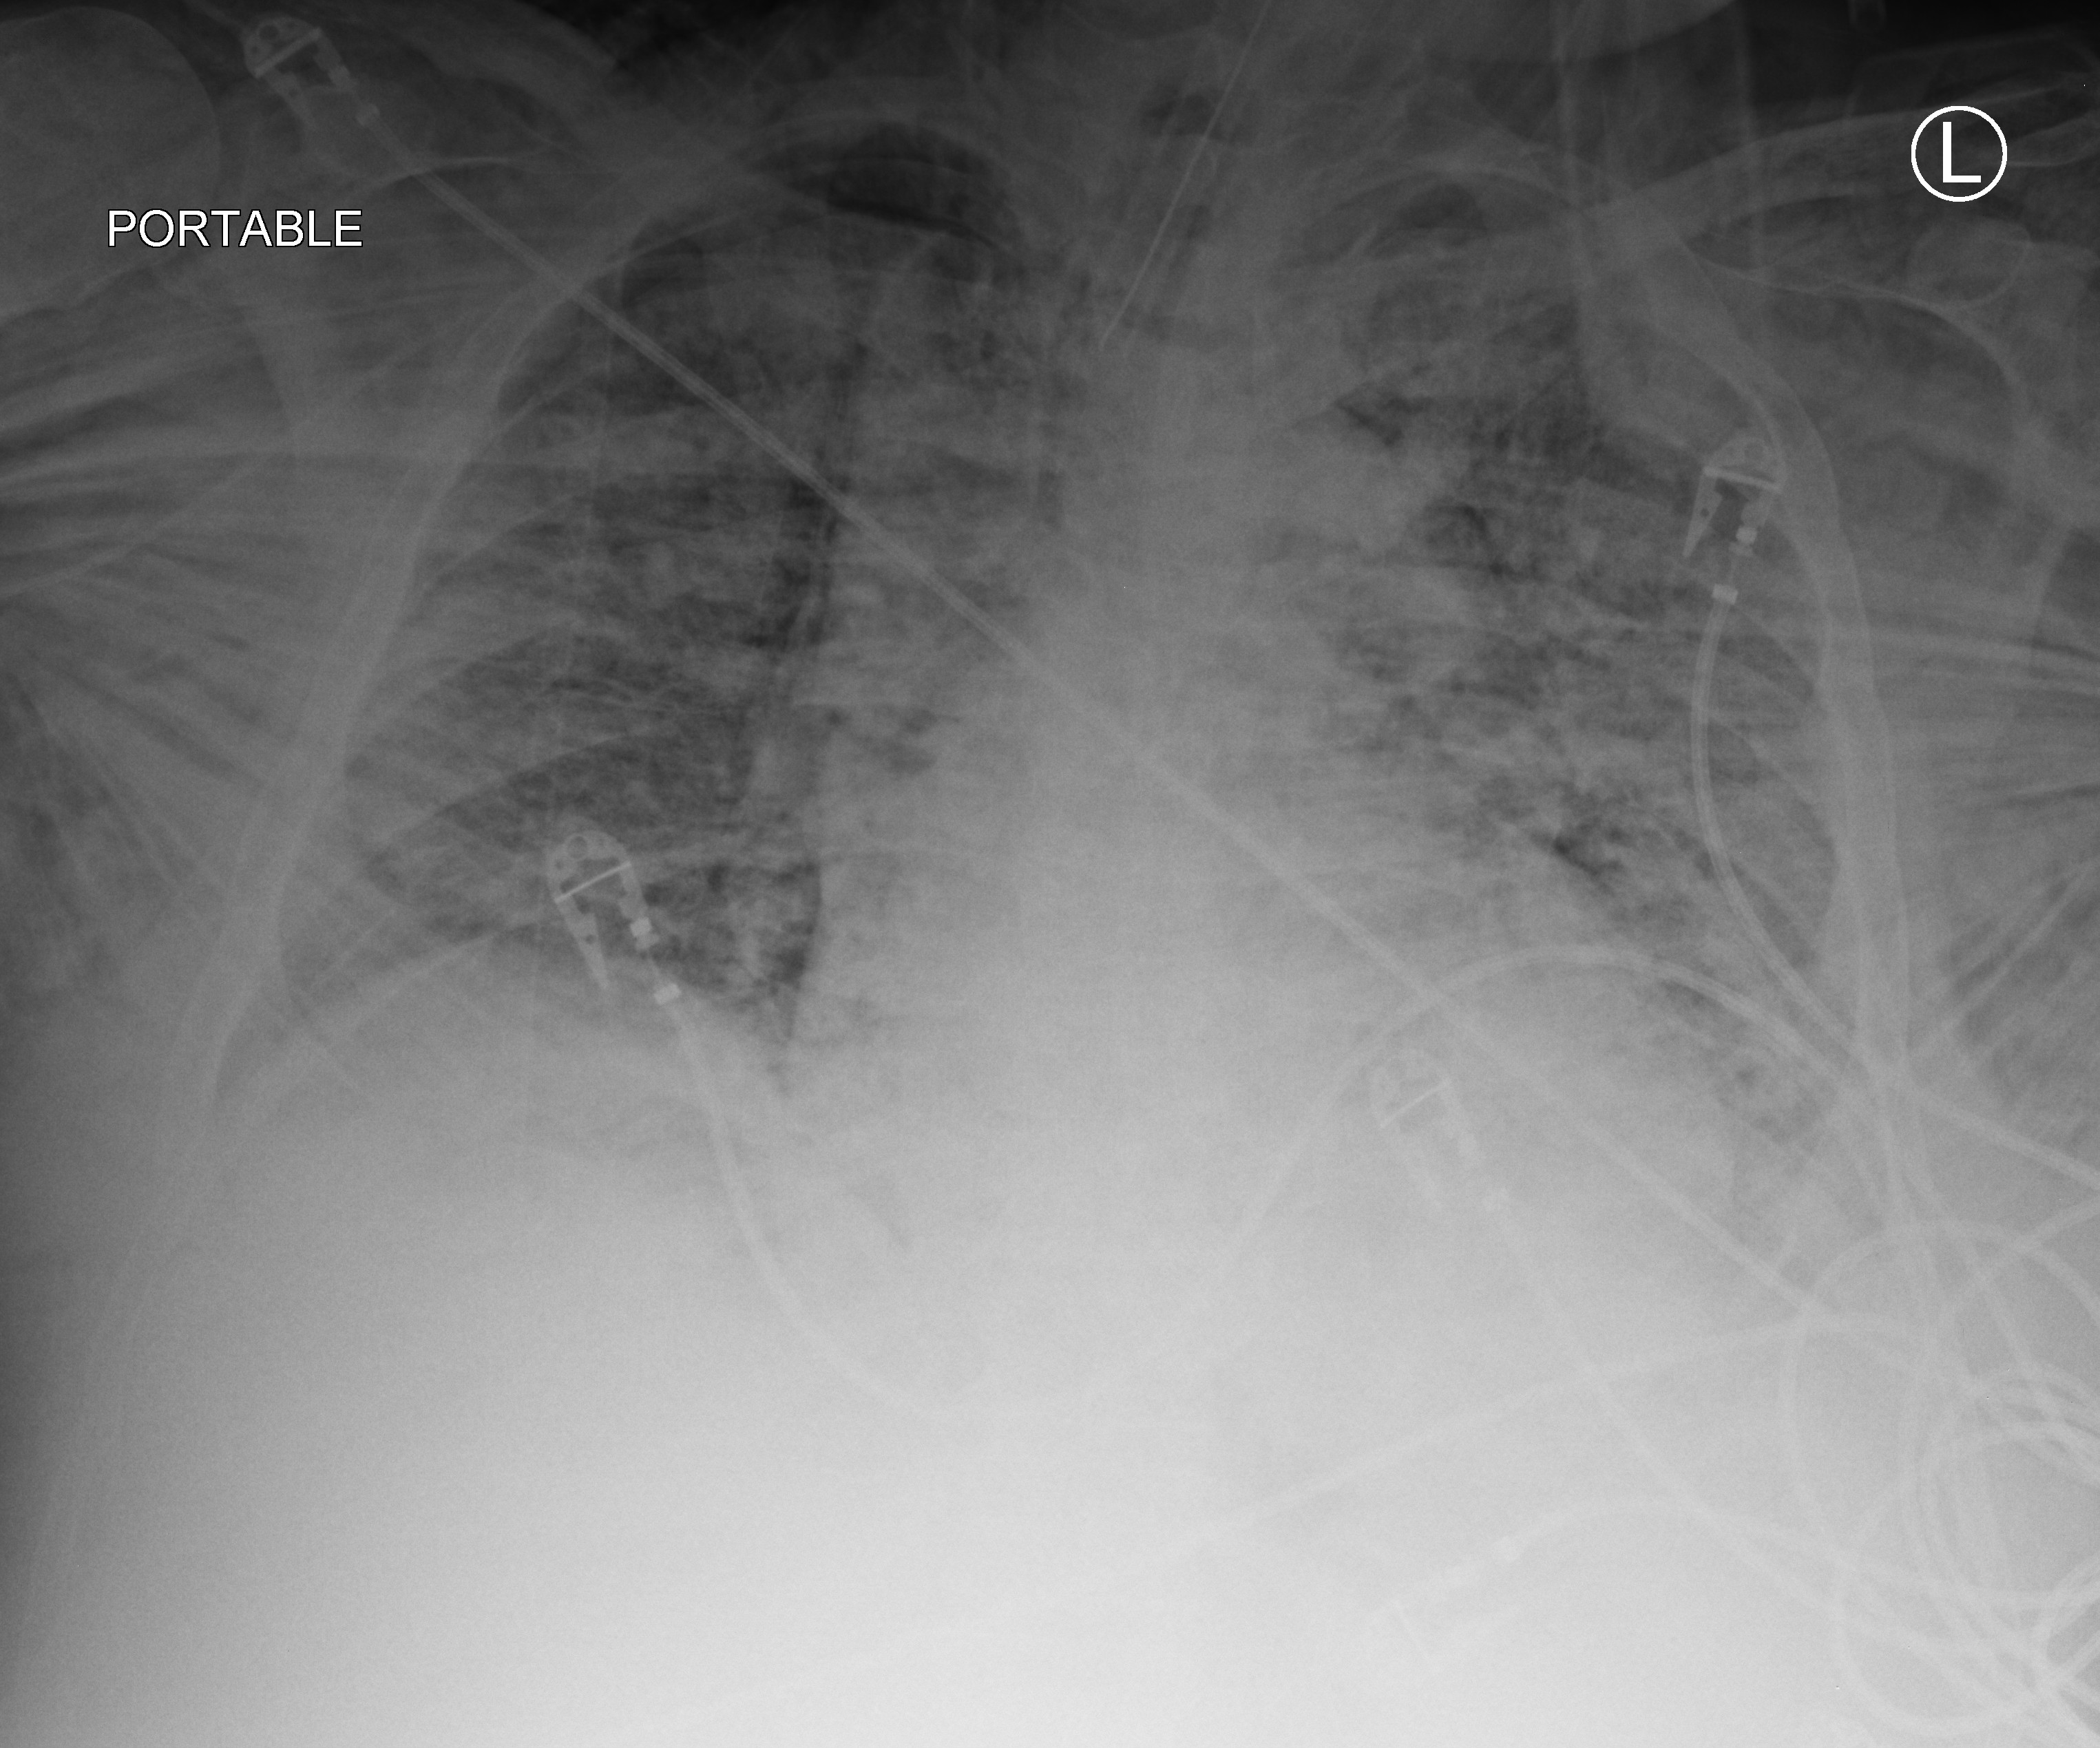
Chest X-ray (portable), anteroposterior (AP) projection. Patient hospitalised with COVID-19, aged 18–59 years.
Hospital-stay facts (about this admission, not read from this image; timing relative to this image not recorded):
- length of hospital stay: 26 days
- admitted to intensive care during this hospital stay: yes